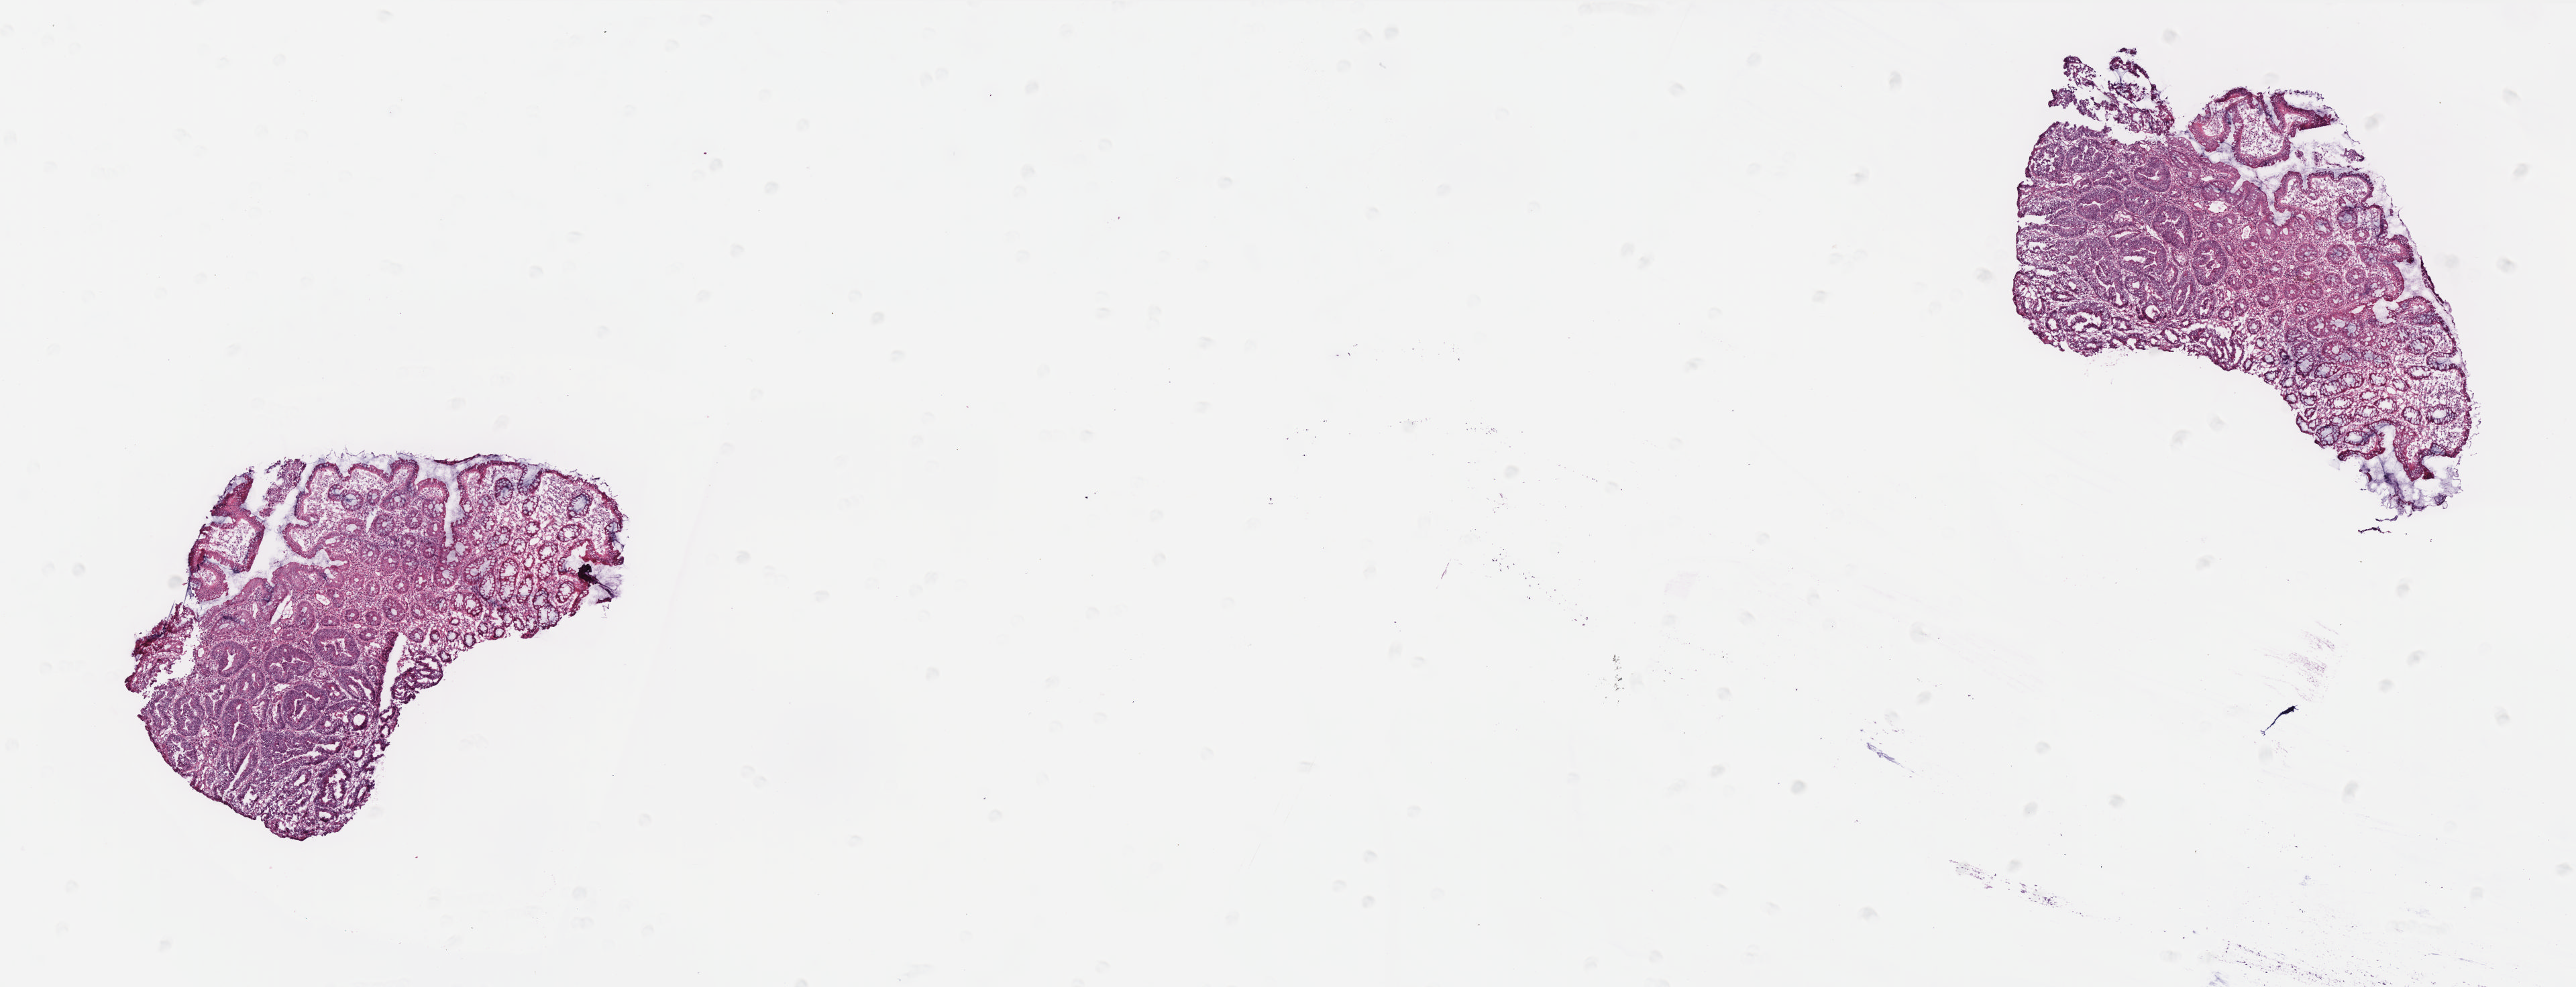
Digitized H&E tissue section (whole slide) — a low-resolution overview of the entire scanned area, about 15.4 x 5.9 mm (from a 40x scan); frozen section; sample: primary tumour, colon. Male patient; age at initial diagnosis 66 years.
Histologic diagnosis: Adenocarcinoma, NOS (sigmoid colon).